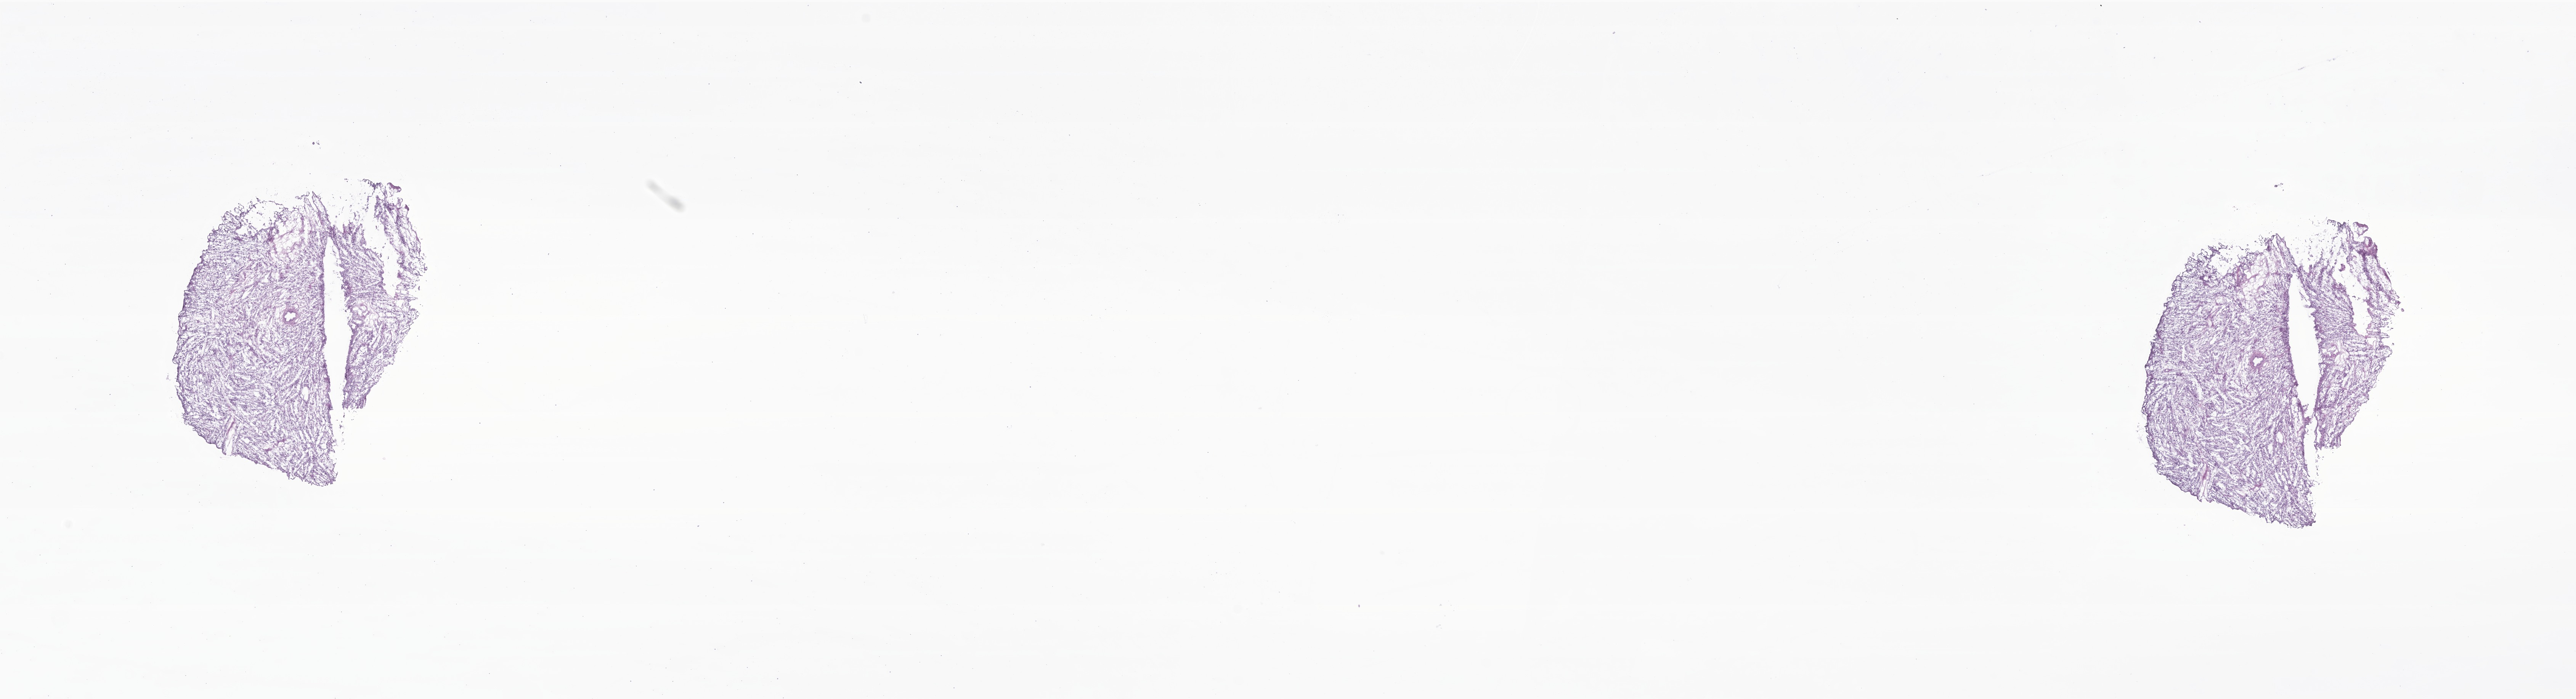
Digitized H&E-stained section of tumor tissue from the testis — whole scanned area (about 28.5 x 7.7 mm) shown as a low-resolution overview; cryosection (OCT / tissue freezing medium). Male patient, age 109 months (9 years 1 month).
- diagnosis: Embryonal rhabdomyosarcoma, NOS